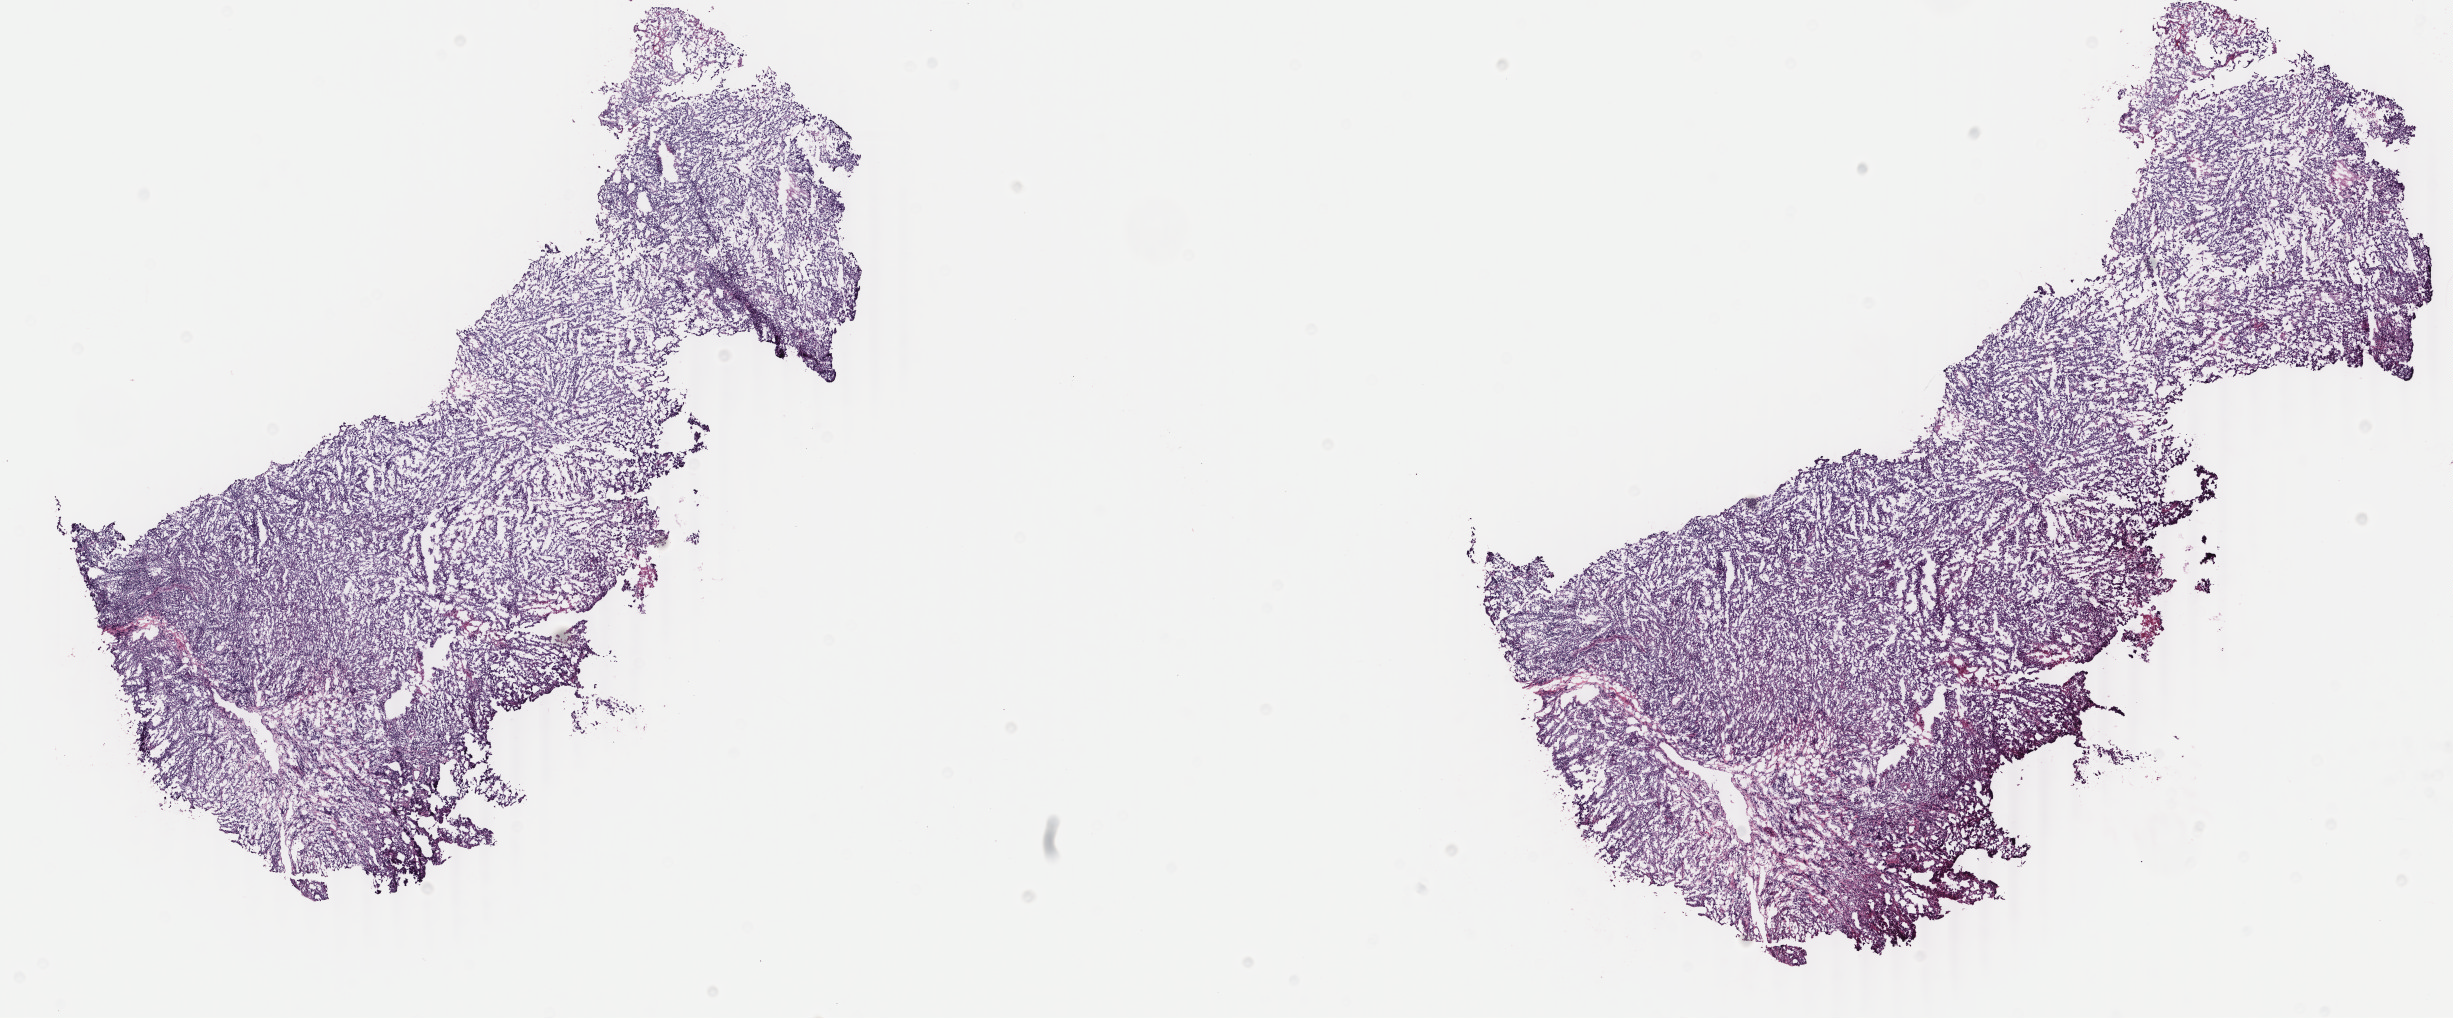
Digitized Hematoxylin and eosin (H&E) stained tissue section (whole slide) — shown as a low-resolution overview of the whole scanned area (about 19.5 x 8.1 mm, acquisition: 40x scan). Frozen section from the top of the tissue portion. Metastatic tumour sample, sampled site not recorded. Patient: female, age at initial diagnosis 50 years. Slide review estimates, as recorded: tumour cells 90%, tumour nuclei 90%, normal cells 0%, stromal cells 8%, necrosis 2%. Infiltration values recorded for this section: lymphocyte infiltration 2%, monocyte infiltration 1%, neutrophil infiltration 1%.
This section: metastatic tumour tissue. Patient diagnosis: Malignant melanoma, NOS.